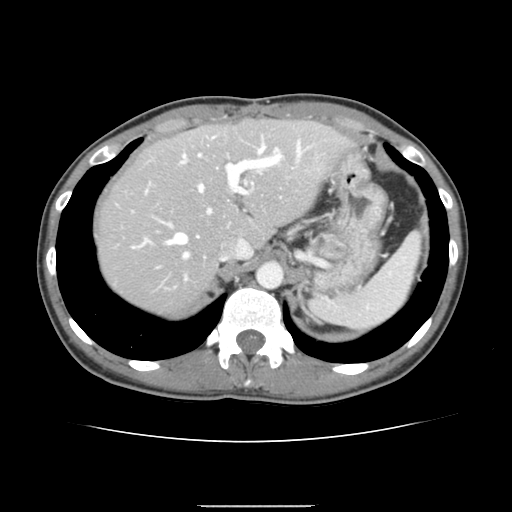
Contrast-enhanced abdominal CT, one axial slice. Position 111 of 150 along the scan axis. Intravenous contrast given. Soft-tissue window (W 400 / L 40 HU). 2.5 mm slice thickness. 512 × 512 image matrix. Female patient, age 32 years. From the clinical record (not read from this slice): diagnosis: colorectal cancer liver metastases, imaged before liver resection; multiple liver metastases: yes; largest metastasis: 0.7 cm.
Annotated regions visible in this slice (manually delineated by an expert):
- hepatic veins: bounding box (x1, y1, x2, y2) in pixels: (157, 150, 282, 281)
- liver: (99, 121, 347, 314)
- planned liver remnant (the part of the liver to remain after resection): (99, 120, 348, 273)
- portal vein (with intrahepatic branches): (133, 136, 307, 248)